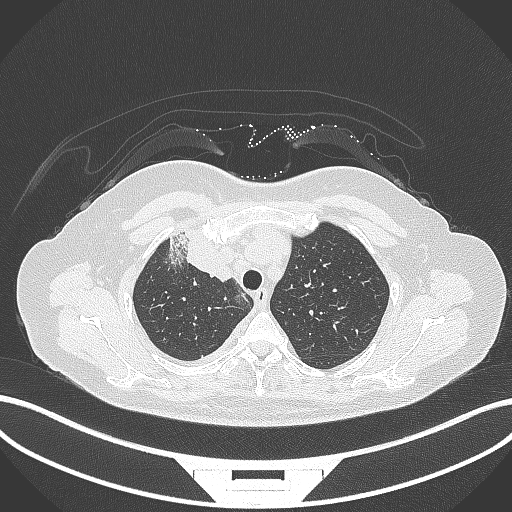
Chest CT, one axial slice; slice 245 of 305 in the series (ordered by position); lung window (W 1500 / L -600 HU); 1 mm slice thickness; 512 × 512 image matrix, field of view 400 × 400 mm. Female patient, age 52 years. From the clinical record (not read from this slice): clinical TNM (as recorded): T3 N1 M1.
Annotated regions visible in this slice (bounding box drawn by a radiologist):
- lung tumour (recorded histology: adenocarcinoma): bounding box [x1, y1, x2, y2] px = [168, 232, 236, 284]